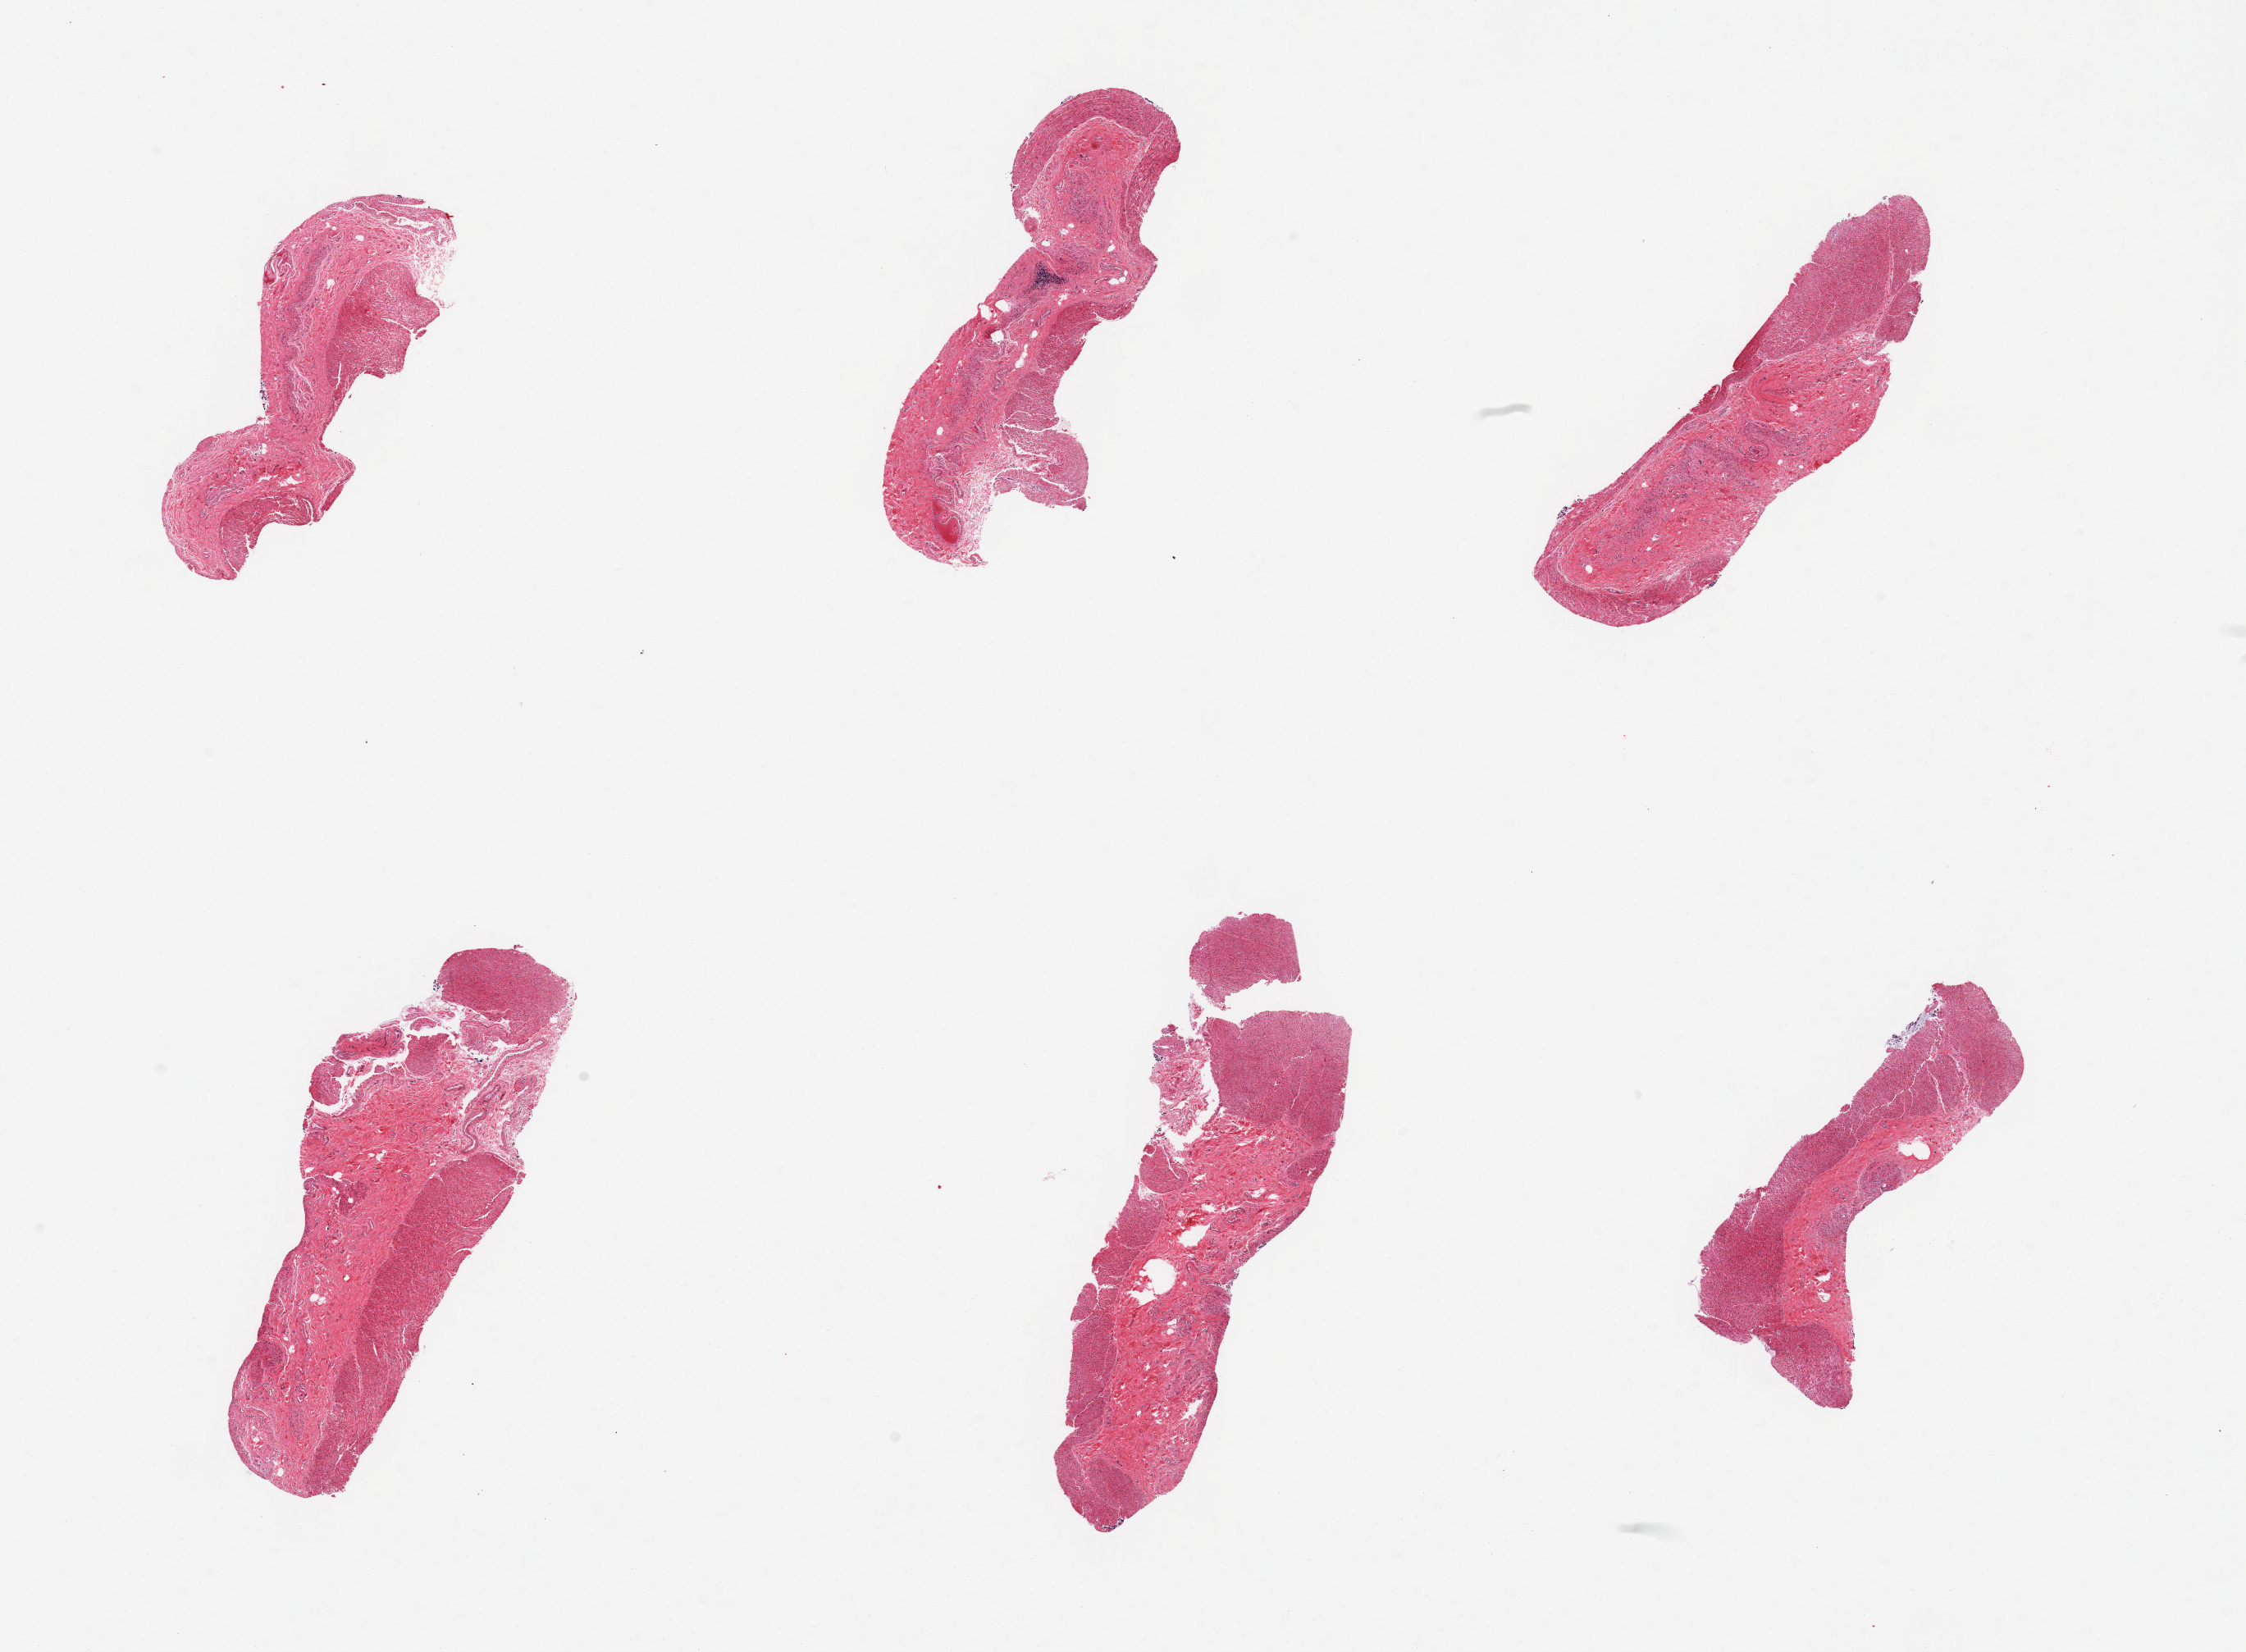
Whole-slide image, haematoxylin and eosin stain, a low-resolution overview of the entire scanned area, about 21.7 x 15.9 mm (slide scanned at 20x). PAXgene-fixed paraffin-embedded (PFPE) section. Section of sigmoid colon (target tissue). Donor tissue sample. Donor sex: male.
* review note (as recorded): 6 pieces; fibrous subucosa occupies 50% of samples